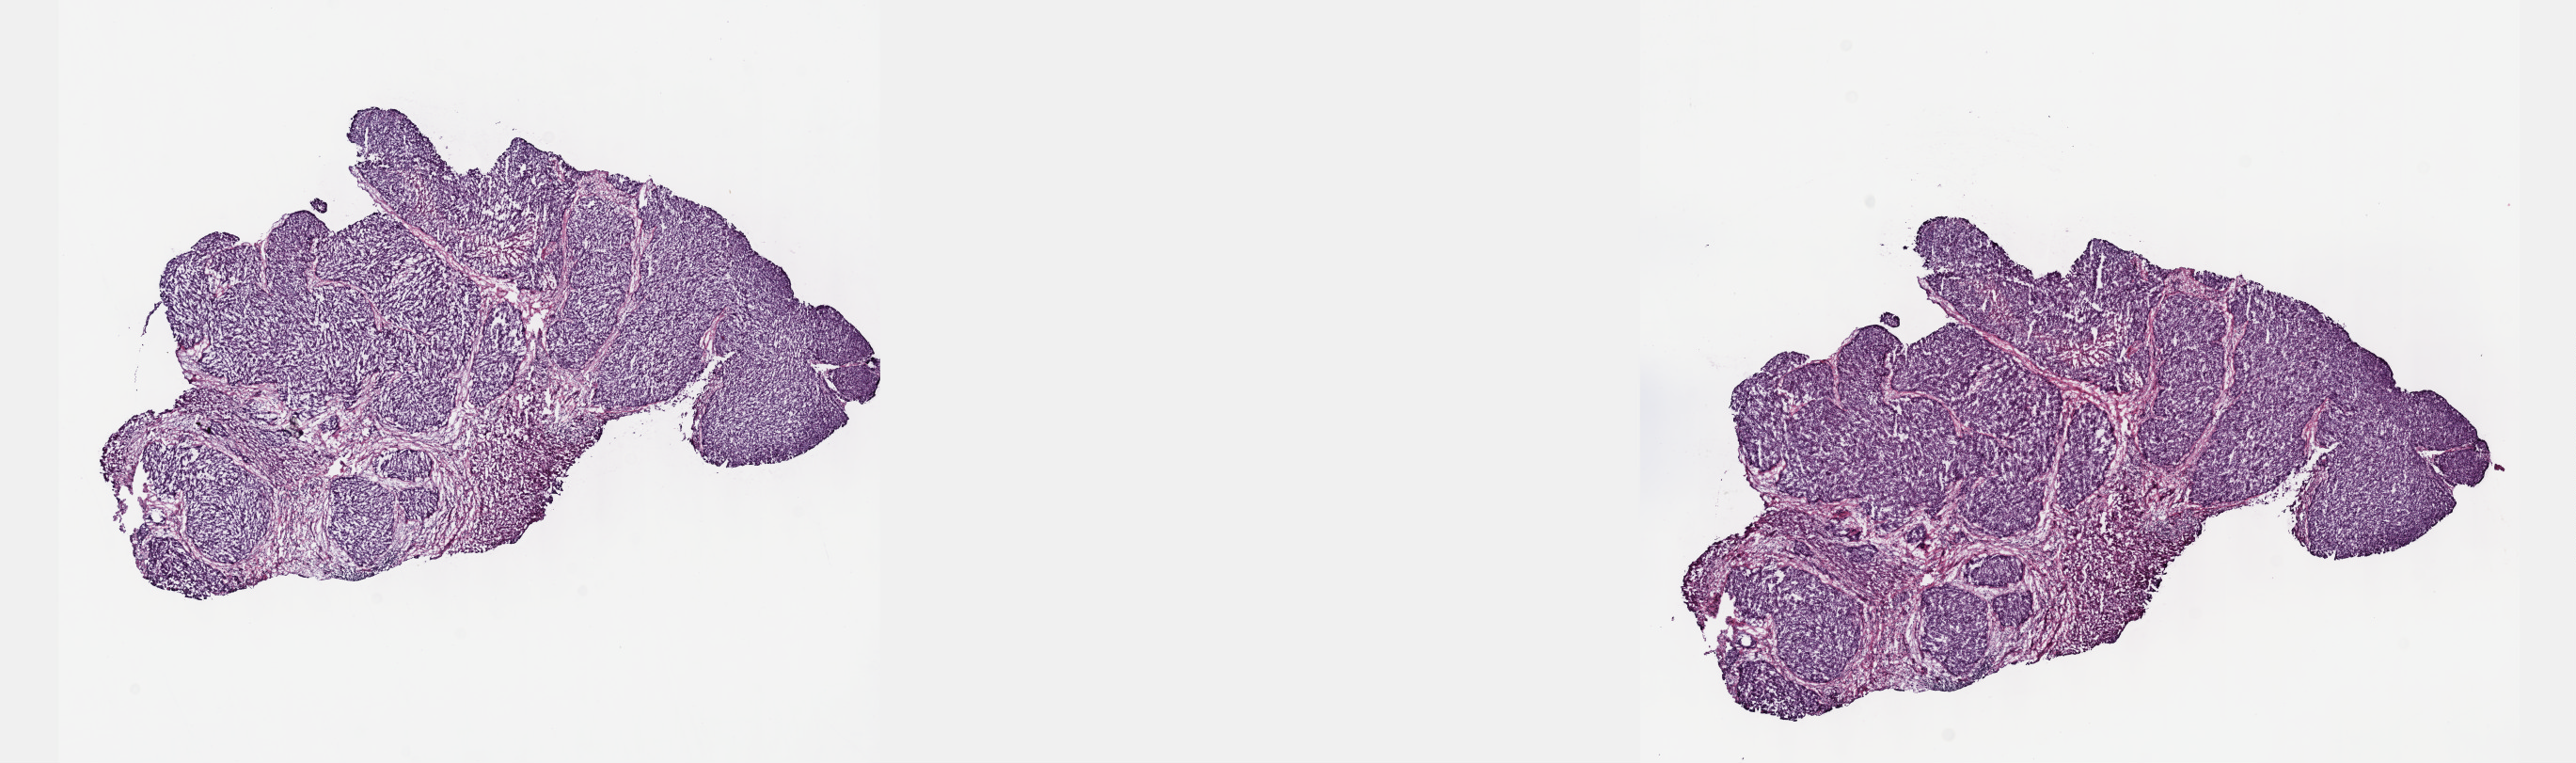
H&E whole-slide image — a low-resolution overview of the entire scanned area, about 22.1 x 6.6 mm; frozen section; primary tumour sample from the liver. Male, age 53 years at initial diagnosis.
Diagnosis: Hepatocellular carcinoma, NOS.